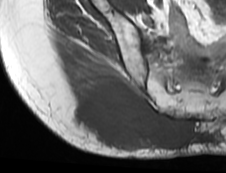
MRI of an extremity soft-tissue mass, one axial slice; slice 46 of 73 in the series (ordered by position); MR volume resampled by the dataset authors to the PET/CT grid (not the native acquisition matrix); 226 × 173 image matrix, field of view 221 × 169 mm. Female patient. Case-level facts recorded for this patient, not image findings: histological type: spindle cell suggestive of myxofibrosarcoma; grade: intermediate; site of the primary tumour: right buttock.
Outlined on this slice (expert contour drawn on MRI and transferred to this co-registered scan by the dataset authors):
- gross tumour volume (mass): bounding box (x1, y1, x2, y2) in pixels: (70, 79, 190, 150)